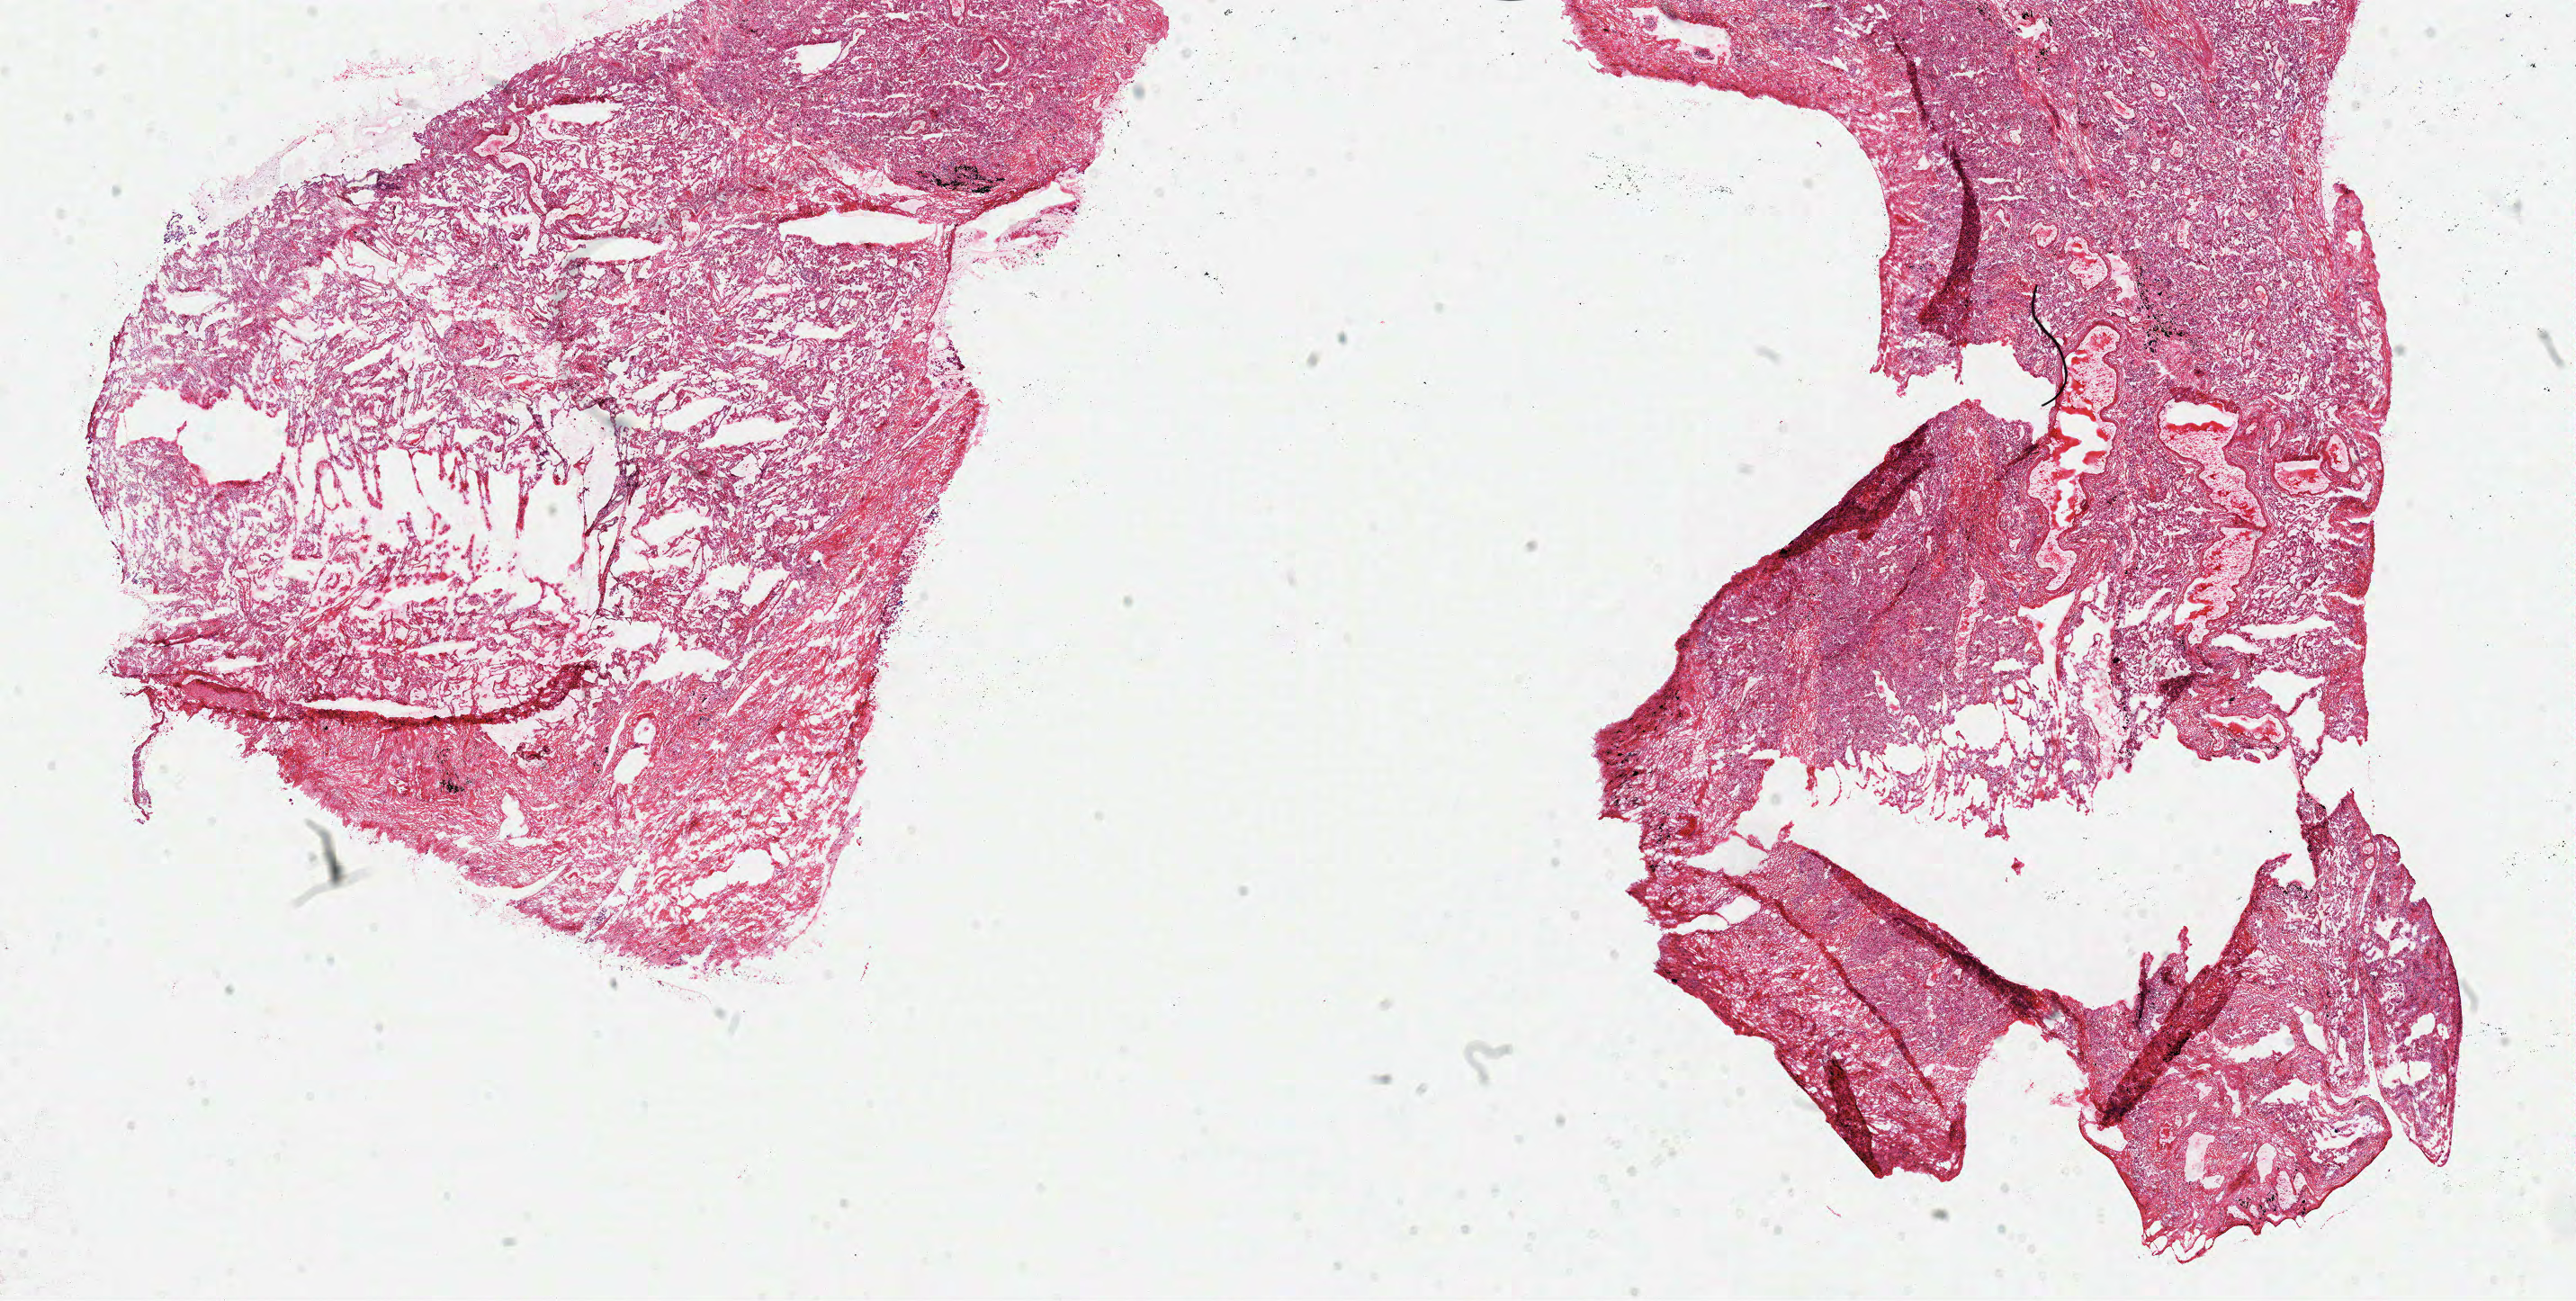
Digitized Hematoxylin and eosin (H&E) stained tissue section (whole slide), shown as a low-resolution overview of the whole scanned area (about 22.5 x 11.4 mm, from a 40x scan), frozen section, solid tissue normal (non-tumour tissue) sample from the lung. Patient: male, age at initial diagnosis 75 years.
This section: solid tissue normal (non-tumour) sample from the same patient. Patient diagnosis: Adenocarcinoma, NOS (upper lobe, lung).